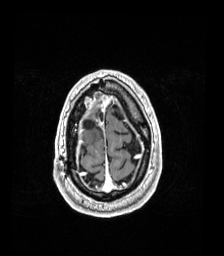
Brain MRI from a brain-tumour surgery series, one axial slice; position 29 of 192 along the scan axis; T1-weighted post-contrast; 1 mm slice thickness; 224 × 256 image matrix. Case-level facts recorded for this patient, not image findings: histopathology: Astrocytoma; WHO grade: 4; IDH mutation: yes.
Structures marked on this image (expert manual segmentation):
- previous resection cavity: bounding box <83,120,95,130> (left, top, right, bottom; pixels)